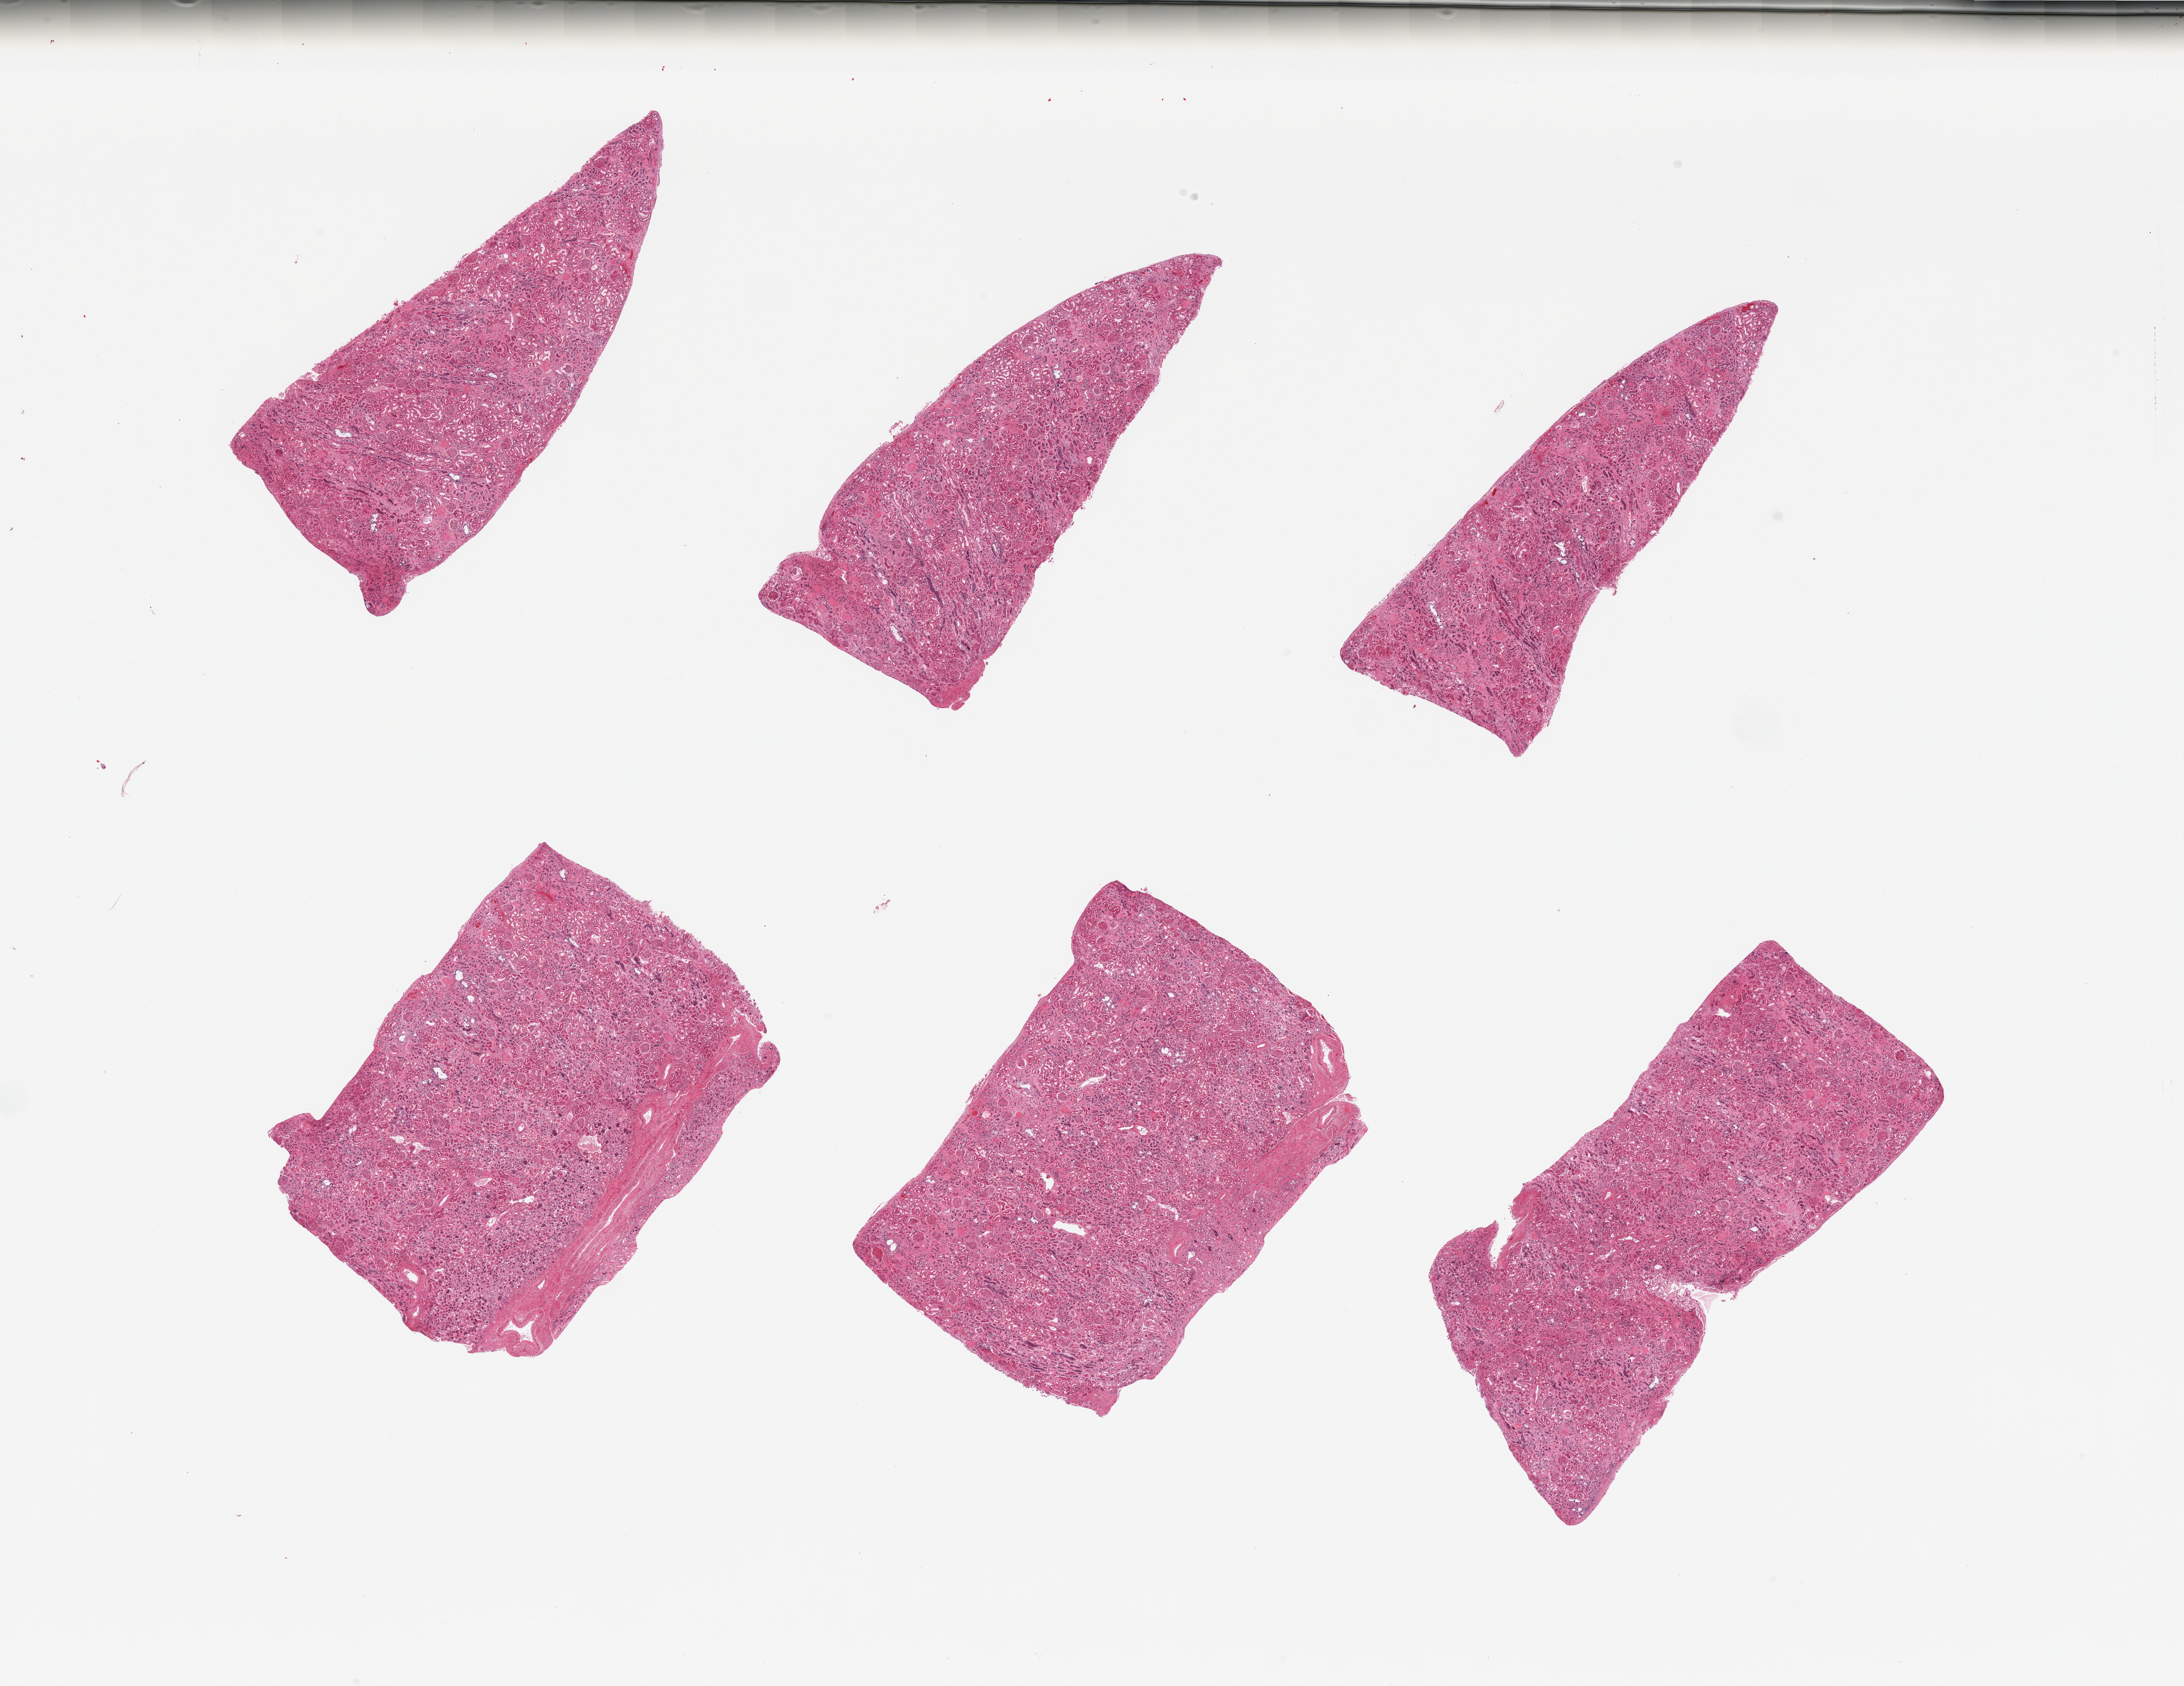
H&E whole-slide image — low-resolution overview of the scanned area, about 30.5 x 23.6 mm (from a 20x scan). PAXgene-fixed paraffin-embedded (PFPE) section. Section of renal cortex (target tissue). Donor tissue sample. Donor: male.
* review note (as recorded): 6 pieces, glomeruli present in call sections